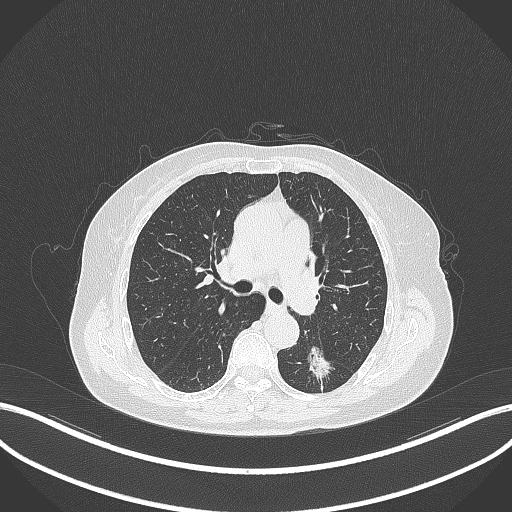
Chest CT, one axial slice; position 183 of 352 along the scan axis; reconstruction kernel B70f; 120 kVp; lung window (W 1500 / L -600 HU); 1 mm slice thickness; 512 × 512 image matrix. Female patient, age 70 years. From the clinical record (not read from this slice): clinical TNM (as recorded): T1c N0 M0.
Structures marked on this image (rectangle marked by the reading radiologist):
- lung tumour (recorded histology: adenocarcinoma): box from (x=301, y=338) to (x=339, y=382) px